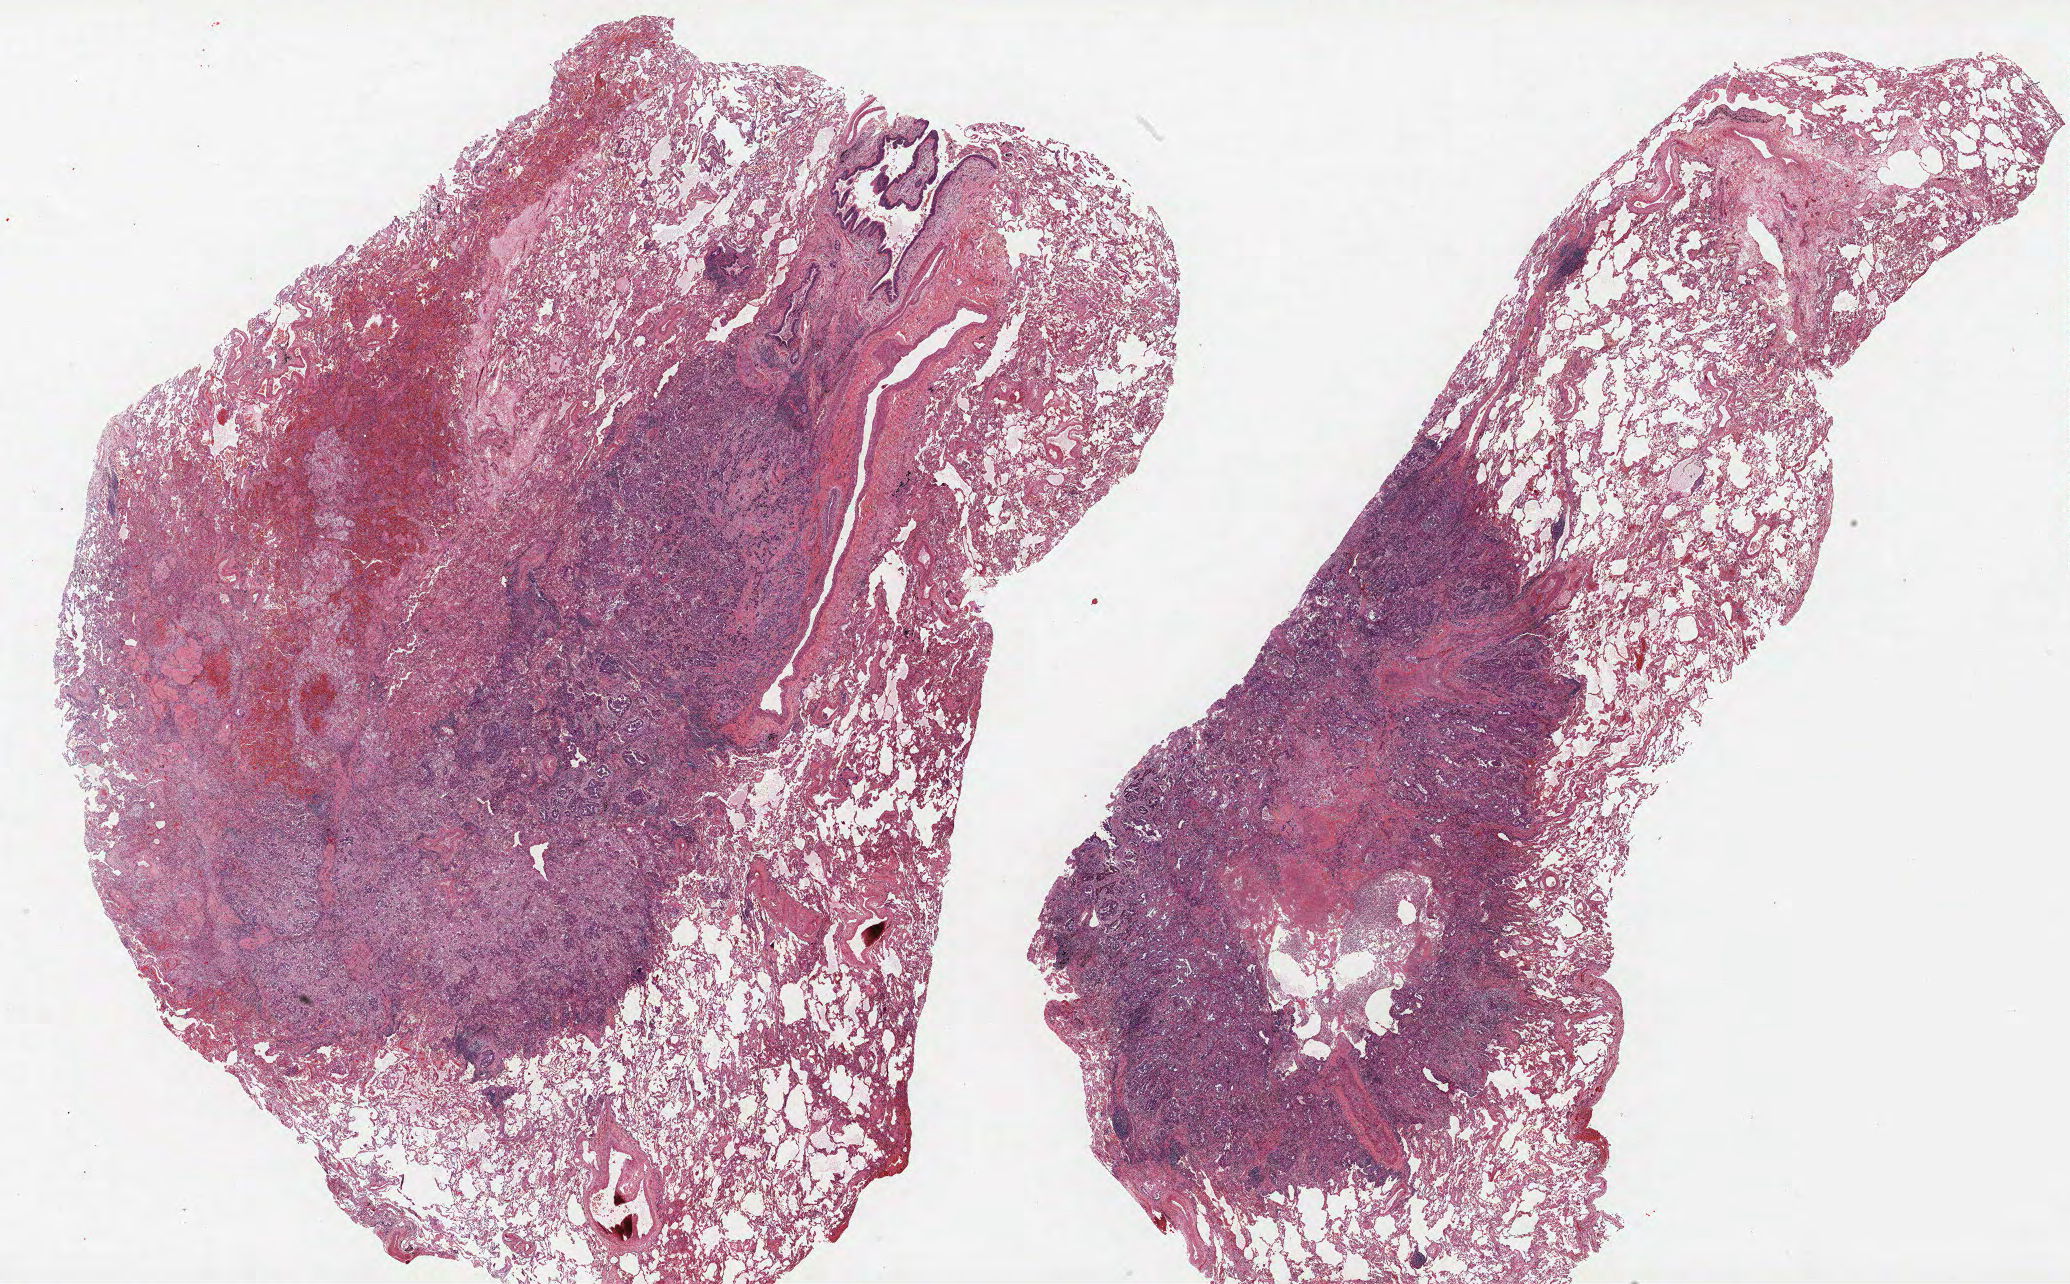
Whole-slide histology image, Hematoxylin and eosin (H&E) stained, whole scanned area (about 33.1 x 20.5 mm) shown as a low-resolution overview, FFPE section, lung. Male, age 69 at enrolment. Current smoker at enrolment. Grade: moderately differentiated (G2).
Participant's lung-cancer diagnosis: Adenocarcinoma, NOS (ICD-O-3 8140/3). Tumour size (pathology): 20 mm. Stage (AJCC 6th edition): IIA. Primary tumour location (clinical record): right upper lobe.